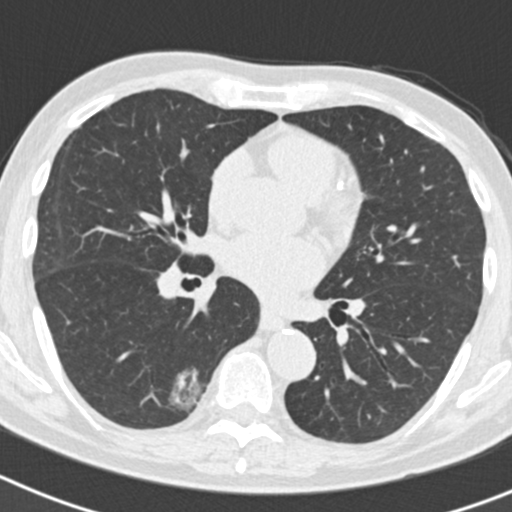
Low-dose screening chest CT, axial slice, second screening round (one year after baseline), lung window (W 1500 / L -600 HU), 512 × 512 image matrix. Male participant, aged 70 years at enrolment. Current smoker at enrolment.
• Expert-annotated lung lesion, bounding box (x1, y1, x2, y2) in pixels: (127, 364, 204, 431).
• The screening reader recorded 5 non-calcified nodules or masses ≥4 mm on this exam (right lower lobe, right lower lobe, right upper lobe, right upper lobe, left upper lobe); which of them this box marks is not recorded.
• Official screen result: positive, other.